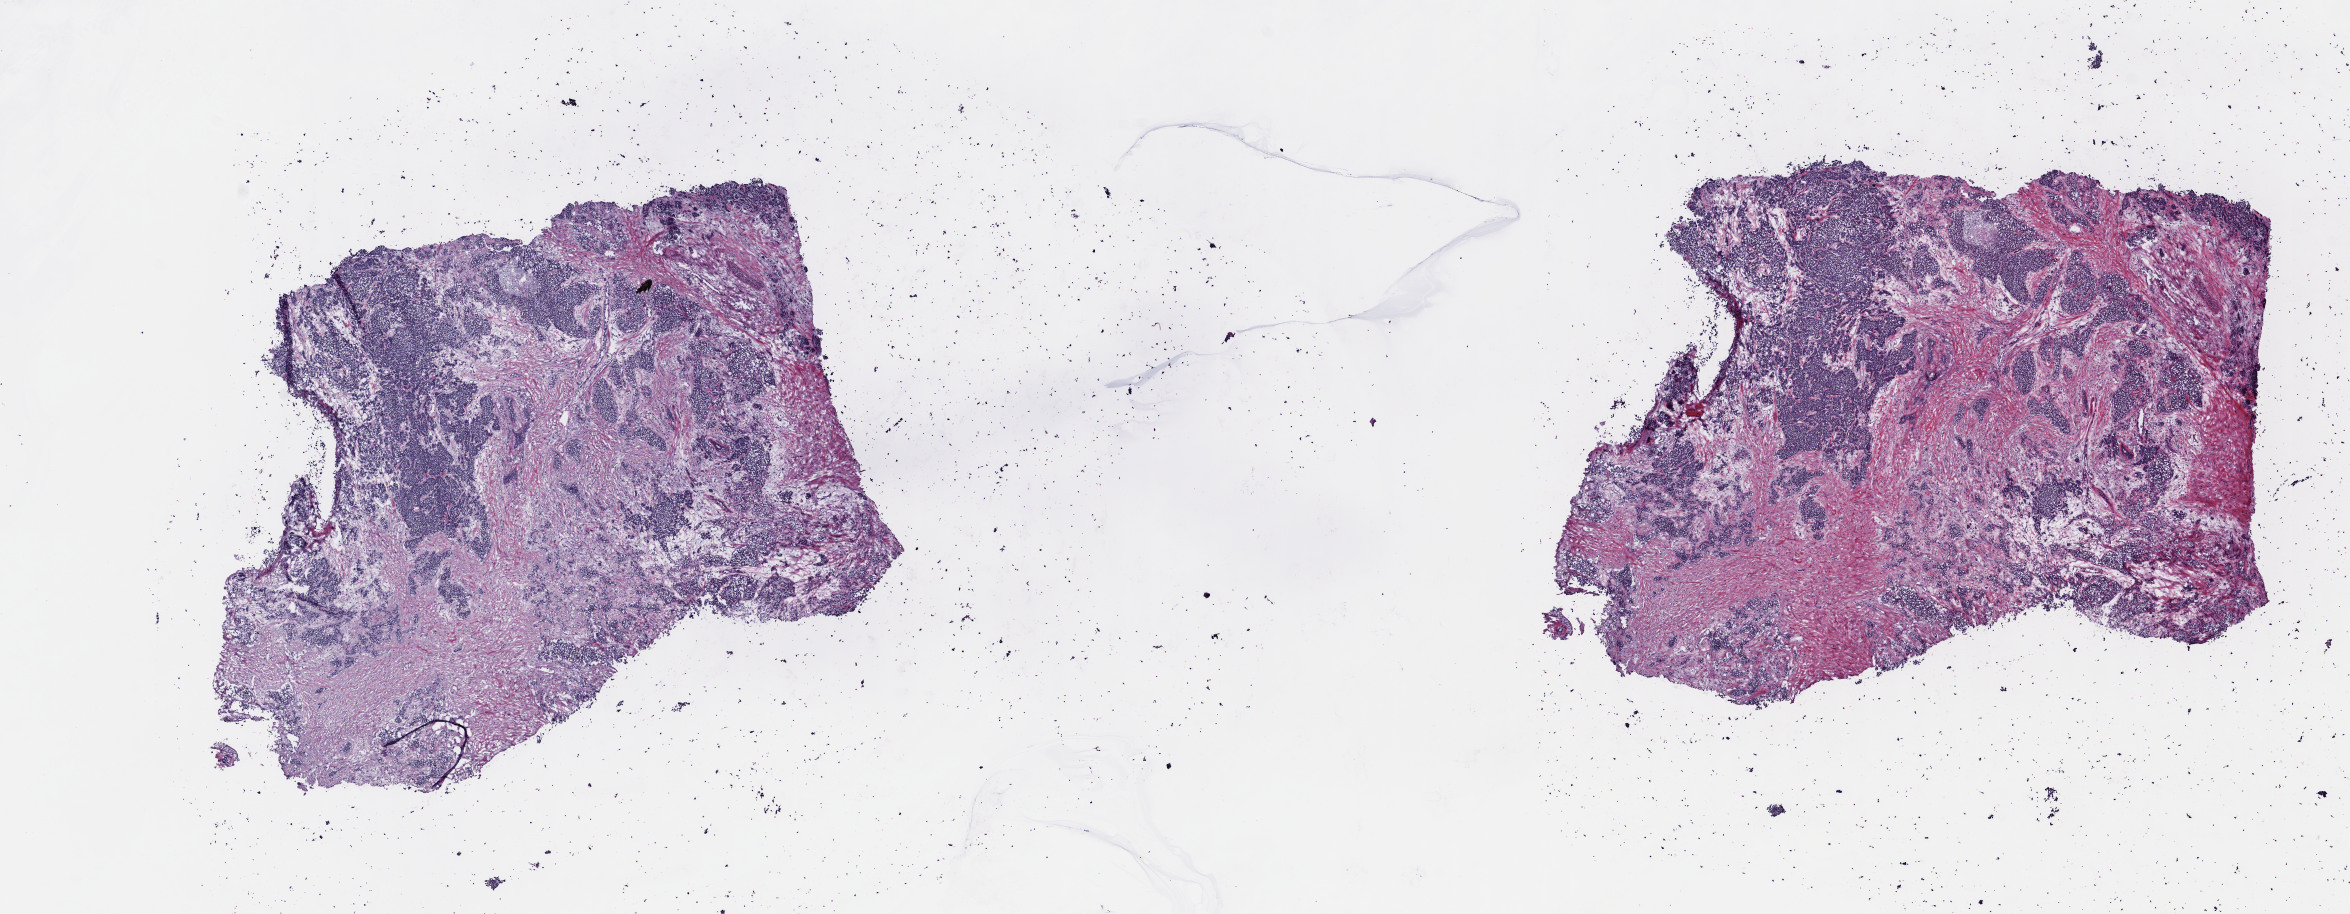
H&E whole-slide image — shown as a low-resolution overview of the whole scanned area (about 18.5 x 7.2 mm, from a 40x scan), frozen section, sample: primary tumour, breast. Female patient; age at initial diagnosis 86 years. Composition of this section per pathologist review: tumour cells 90%, tumour nuclei 85%, normal cells 0%, stromal cells 10%, necrosis 0%. Inflammatory infiltration, as recorded: lymphocyte infiltration 0%, monocyte infiltration 0%, neutrophil infiltration 0%.
AJCC pathologic stage: IIIB (7th edition). Lymph nodes positive (case pathology): 2 of 2 examined. Pathologic diagnosis: Infiltrating duct carcinoma, NOS.